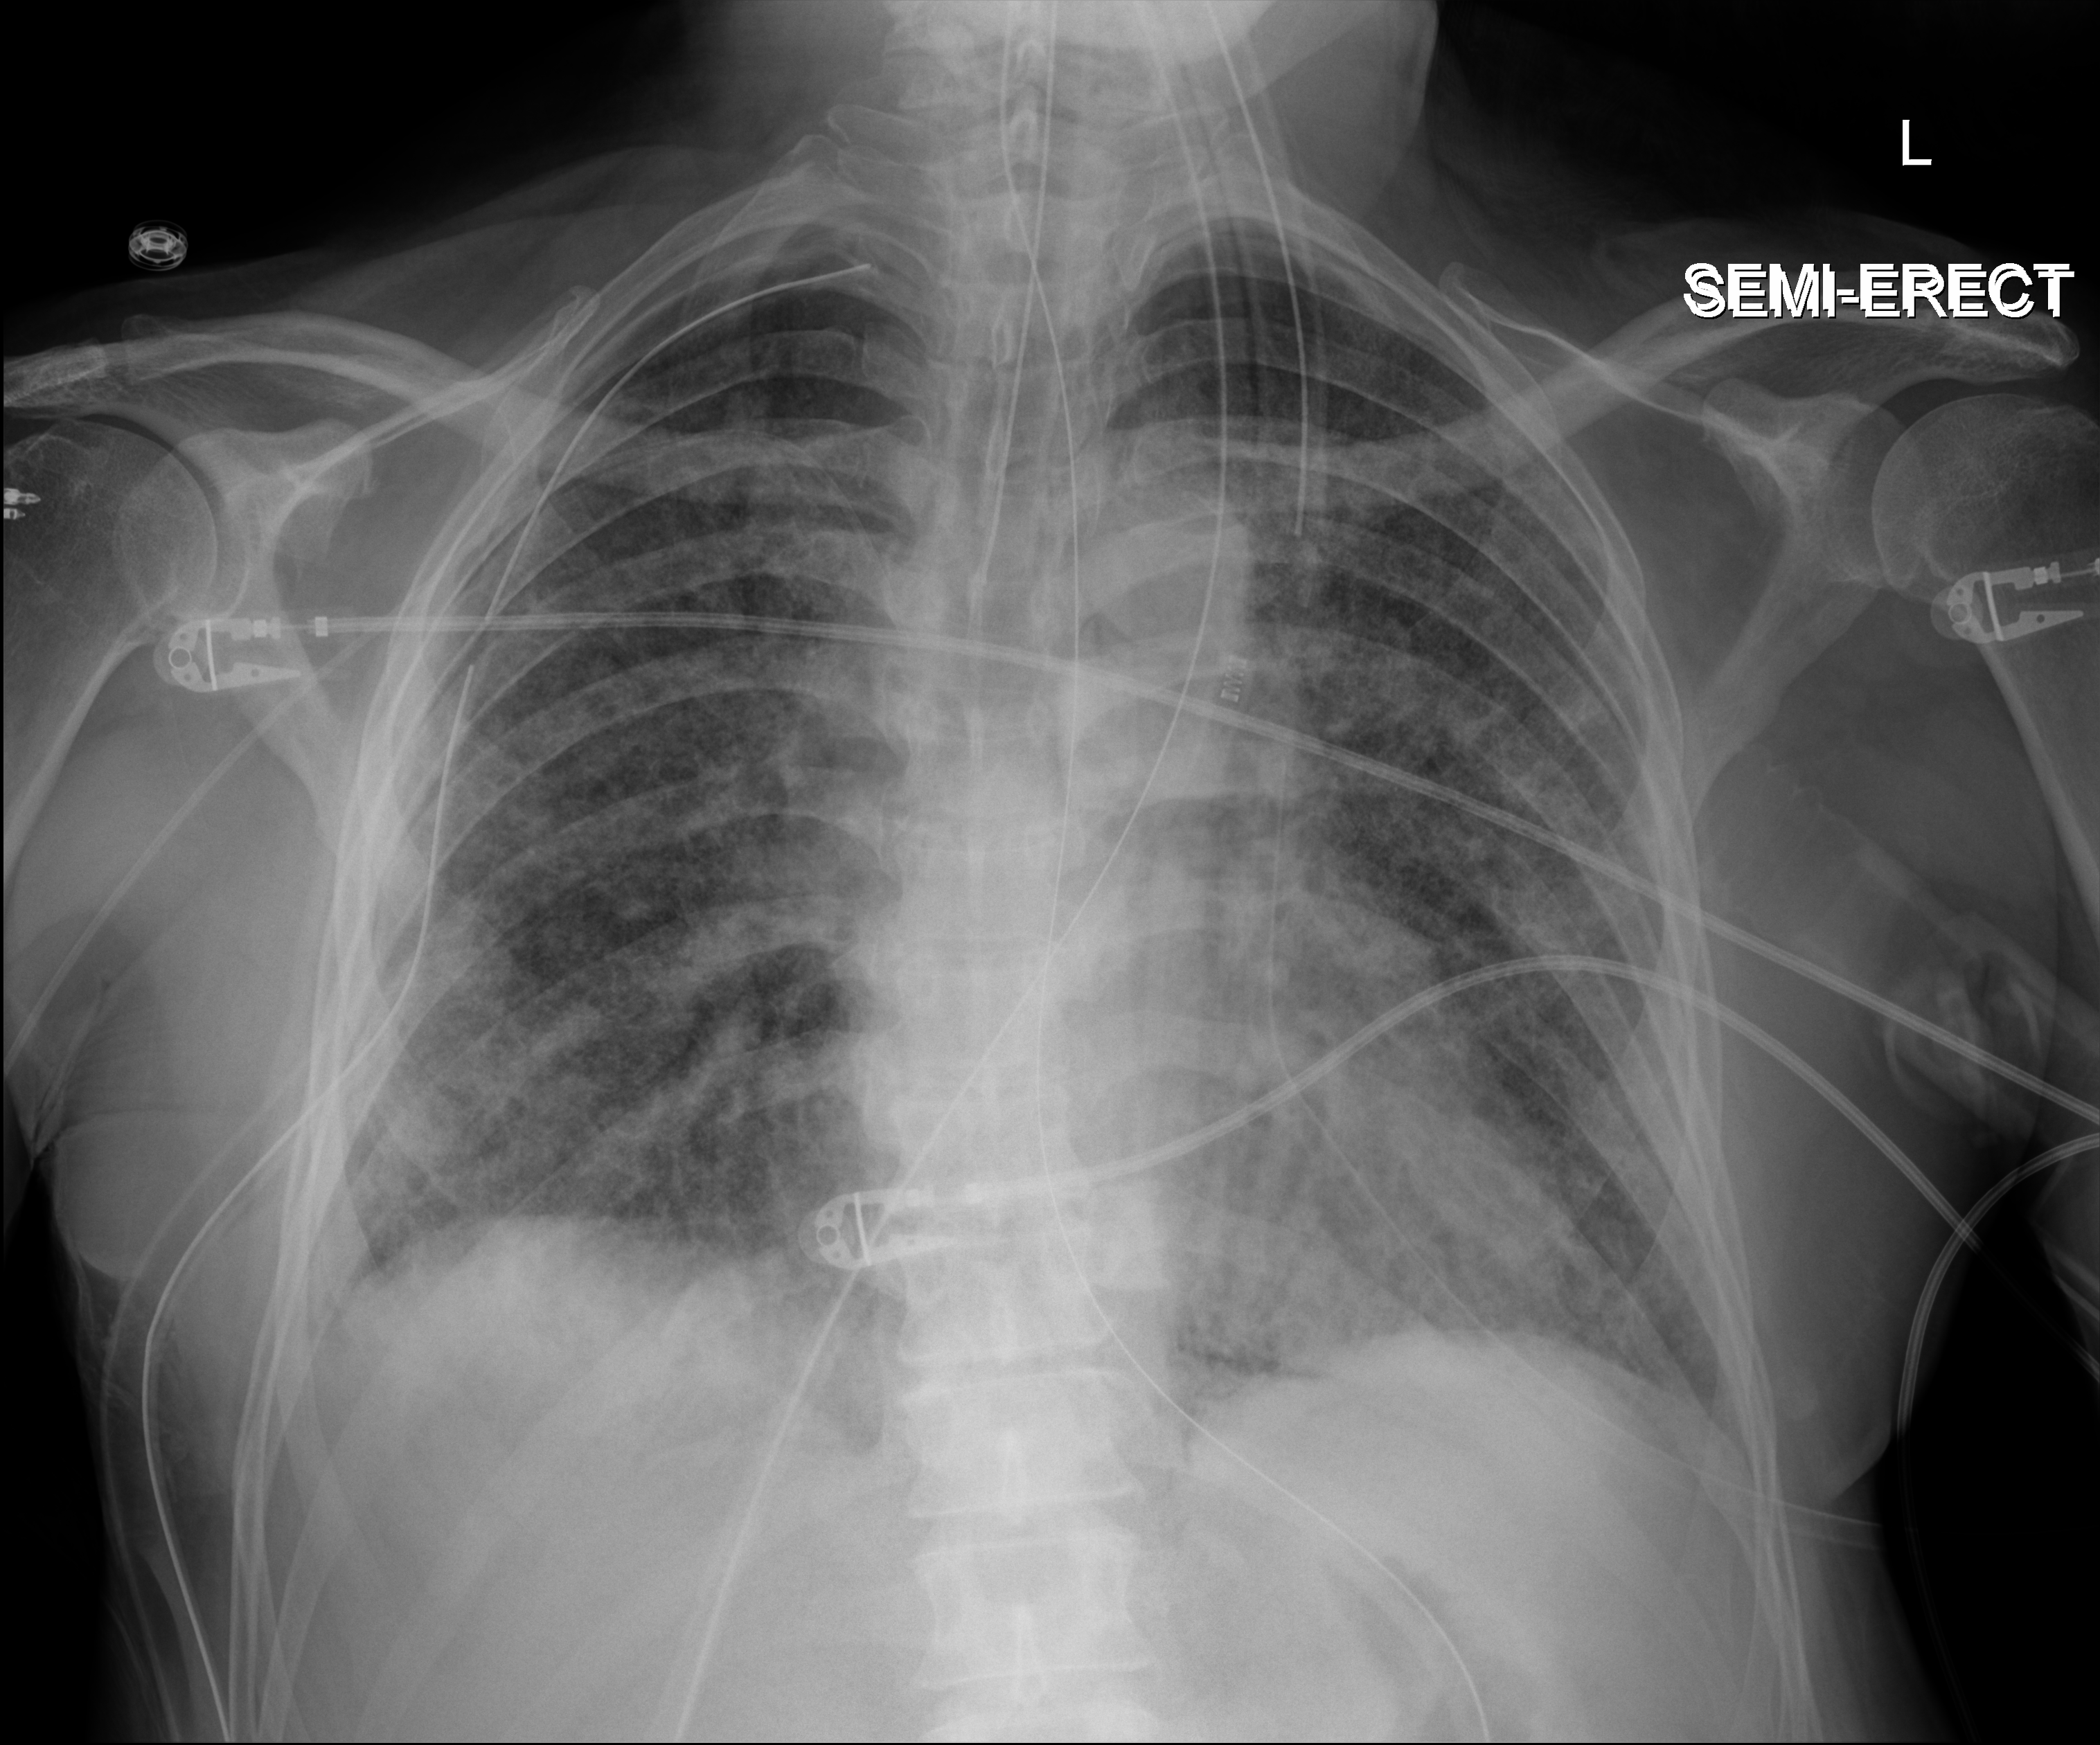
Bedside chest radiograph (digital radiography). Male patient hospitalised with COVID-19, age 60–74 years.
Admission-level facts for this patient (not findings on this image; timing relative to this image not recorded): mechanically ventilated during this hospital stay: yes.